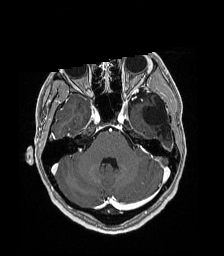
Brain MRI from a brain-tumour surgery series, one axial slice; slice 129 of 192 in the series (ordered by position); T1-weighted post-contrast; 1 mm slice thickness; 224 × 256 image matrix. From the clinical record (not read from this slice): histopathology: Low grade glioma; IDH mutation: no; tumour location: Left Parieto-Occipital Intraventricular.
Outlined on this slice (outlined manually by an expert reader):
- previous resection cavity: box from (x=143, y=98) to (x=170, y=138) px